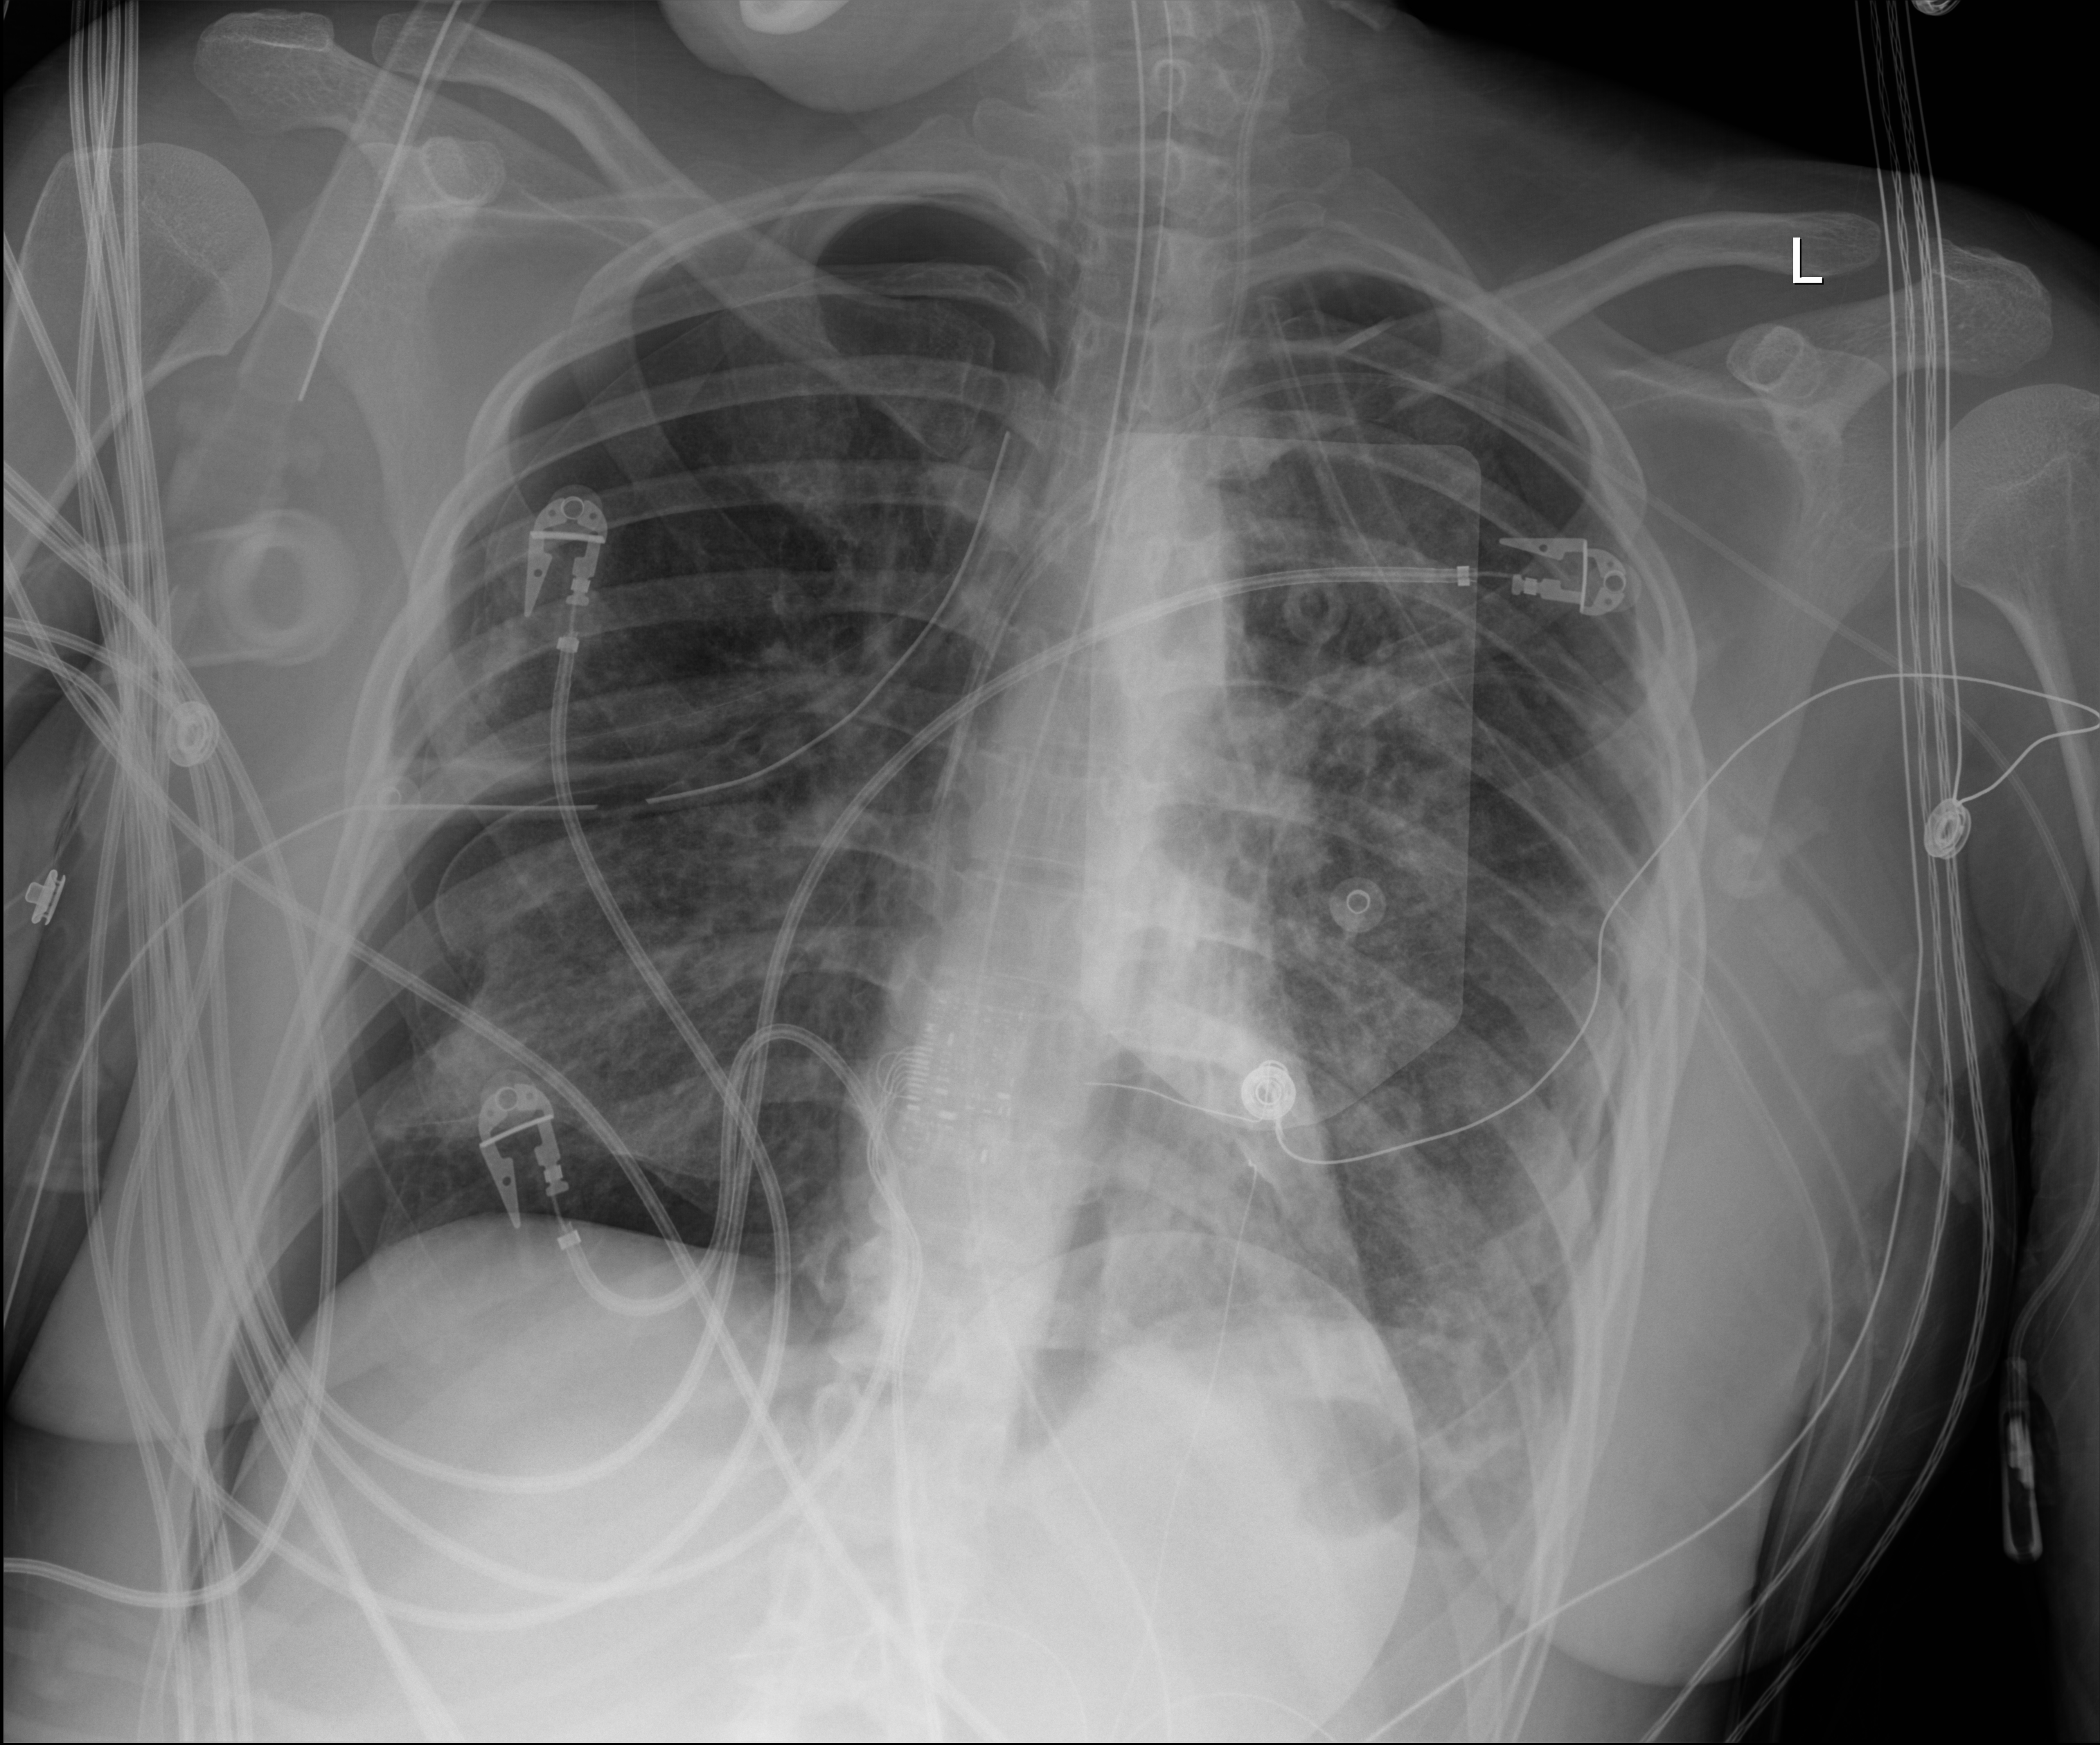
Portable chest radiograph; anteroposterior (AP) projection. Adult patient hospitalised with COVID-19, age 18–59 years.
From the hospital-stay record, not from the radiograph (when in the stay this image was taken is not recorded): admitted to intensive care during this hospital stay: yes; mechanically ventilated during this hospital stay: yes; length of hospital stay: 30 days.